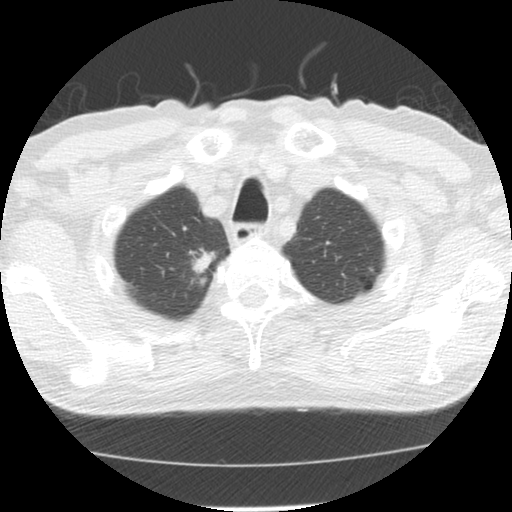
Low-dose screening chest CT, one axial slice. Position 118 of 139 along the scan axis. Reconstruction kernel STANDARD. Lung window (W 1500 / L -600 HU). 2.5 mm slice thickness. 512 × 512 image matrix, field of view 310 × 310 mm.
Outlined on this slice (expert manual segmentation):
- lesion 1 (tumor, upper lobe of right lung): box from (x=189, y=248) to (x=216, y=274) px